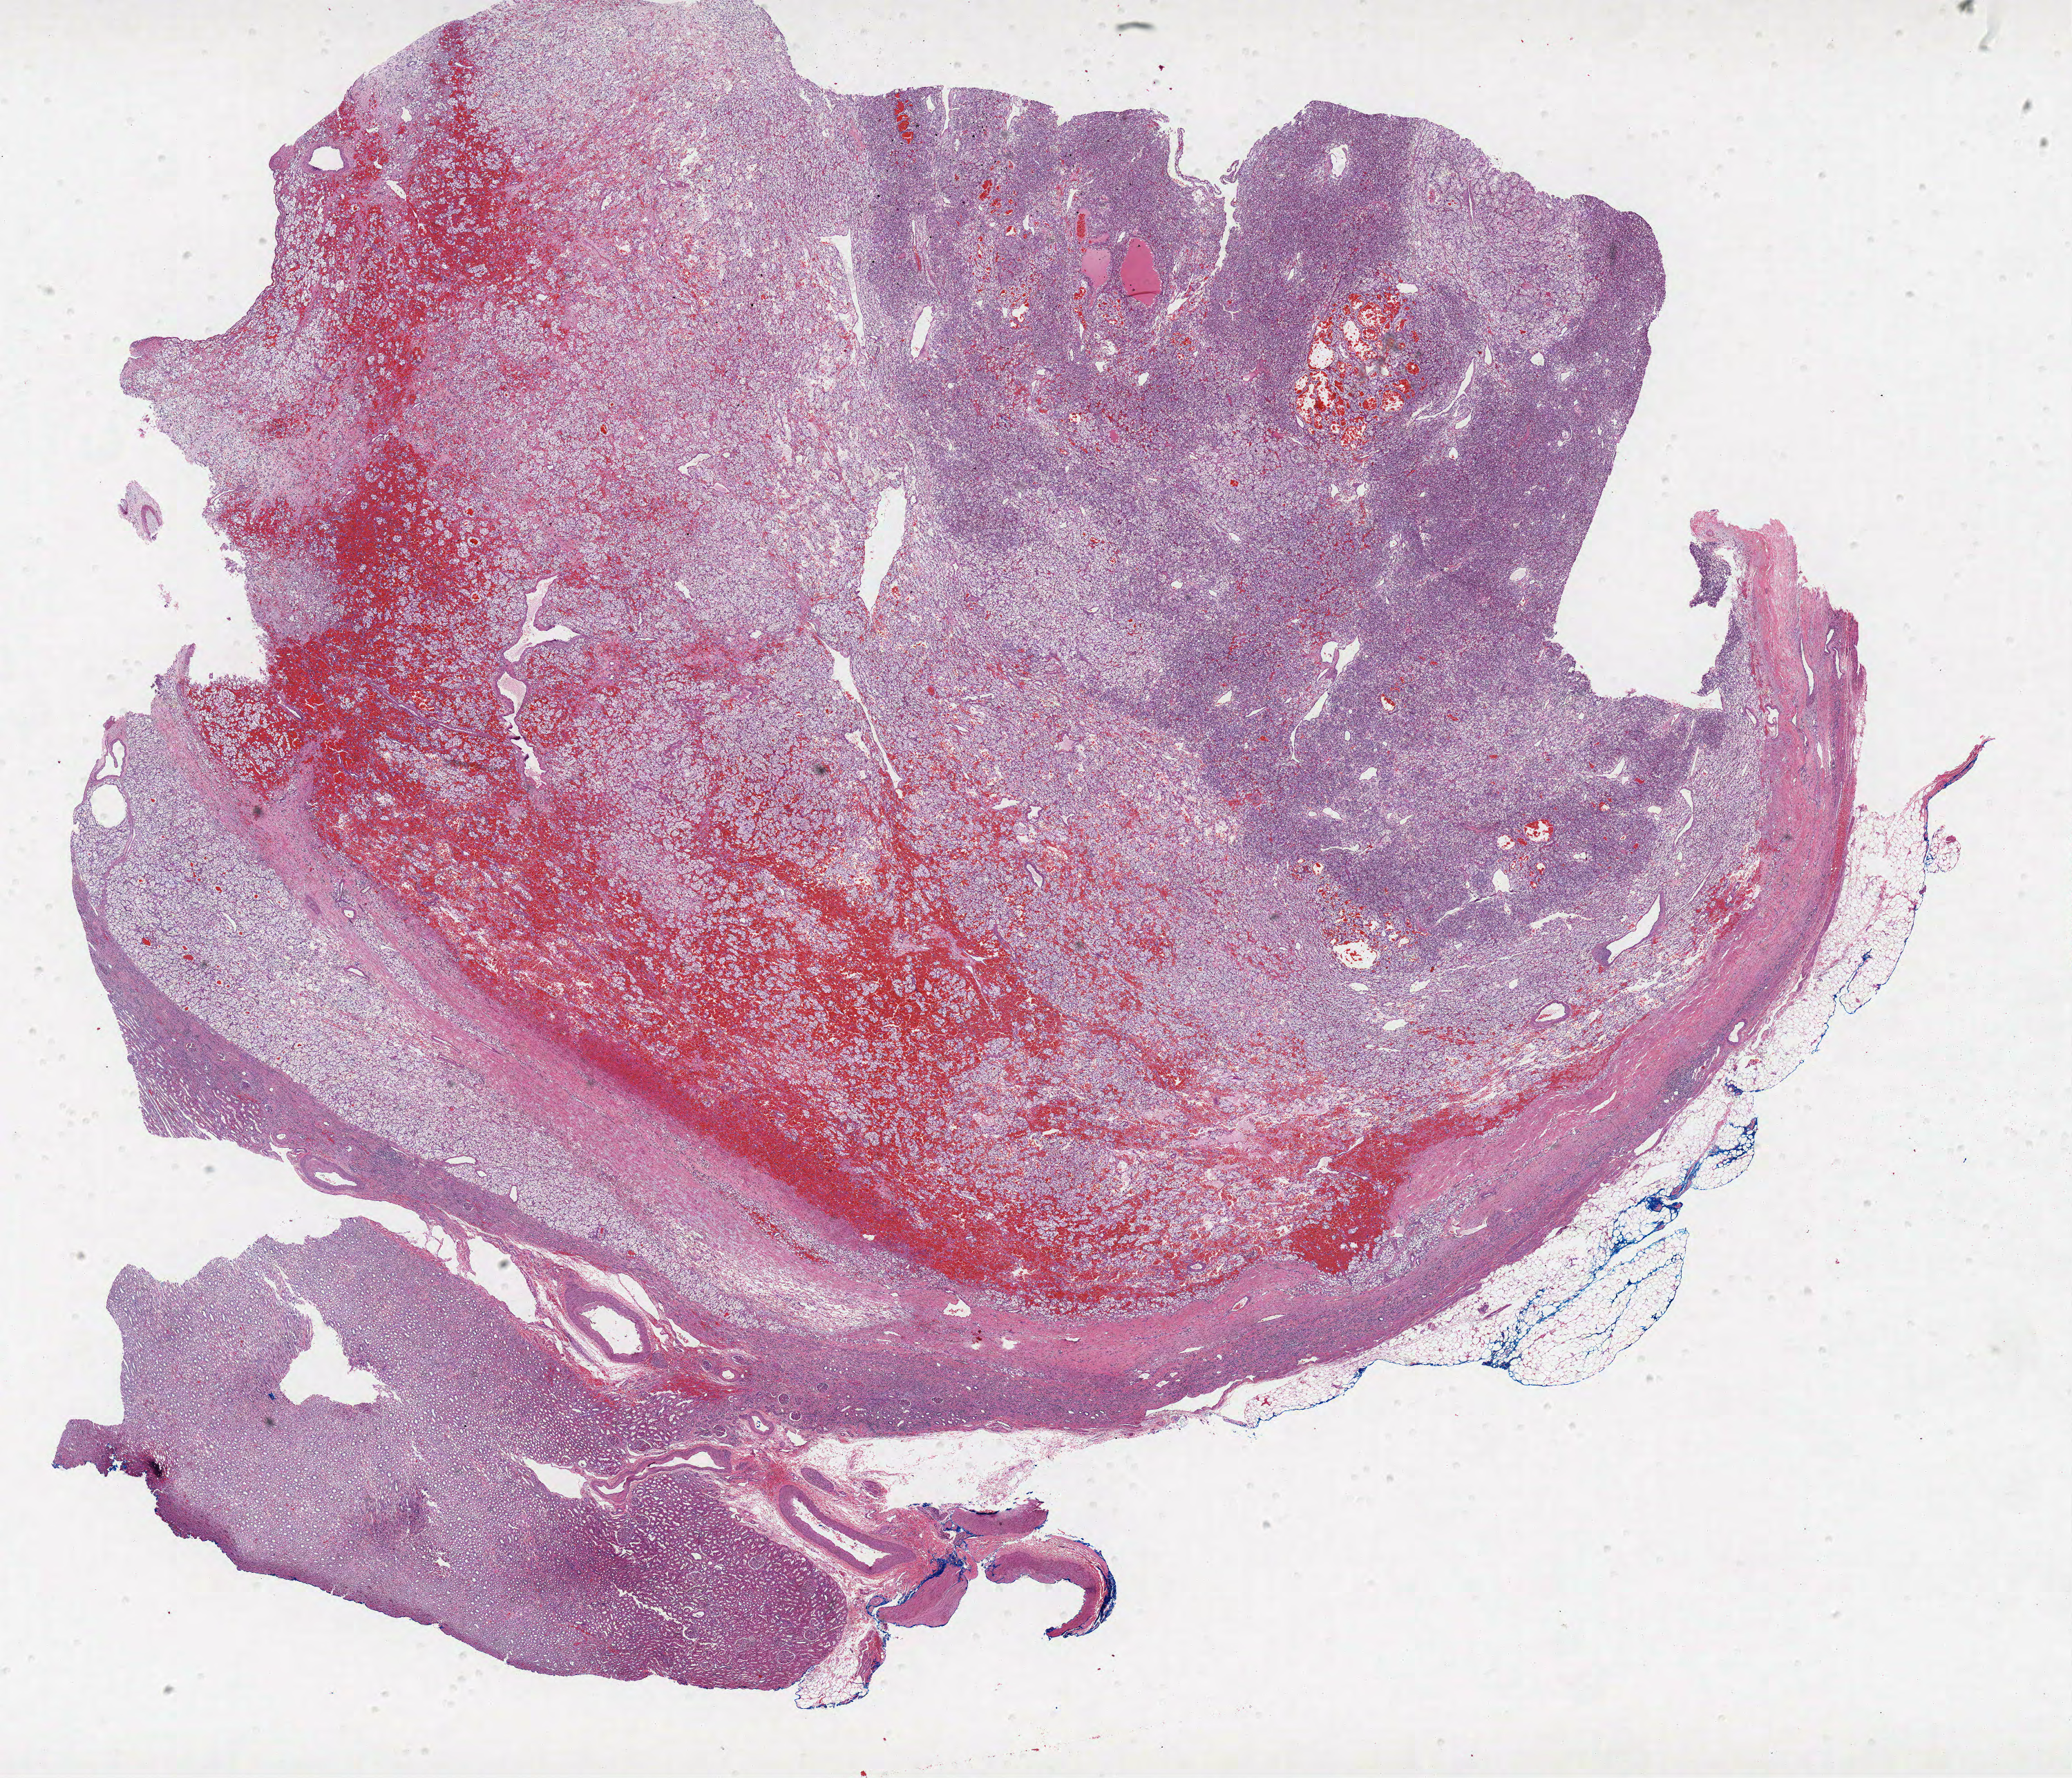
Digitized Hematoxylin and eosin (H&E) stained tissue section (whole slide) — low-resolution overview of the scanned area, about 24.0 x 20.6 mm; formalin-fixed paraffin-embedded (FFPE) diagnostic section; primary tumour sample from the kidney. Female patient; age at initial diagnosis 43 years. Histologic grade: G3 (poorly differentiated).
AJCC pathologic stage: I. Diagnosis: Clear cell adenocarcinoma, NOS.